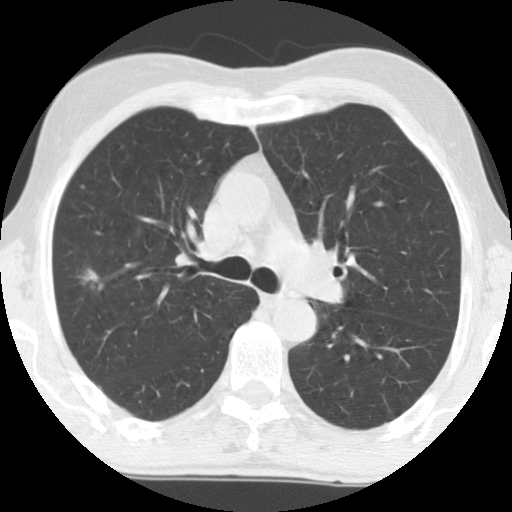
Low-dose screening chest CT, axial slice. Baseline annual screen. Lung window (W 1500 / L -600 HU). Slice 45 of 133 in the series. Male participant, aged 69 years at enrolment.
• Expert-annotated lung lesion, bounding box [x1, y1, x2, y2] px = [57, 256, 116, 311].
• Screening reader's record for this exam (one nodule recorded; not confirmed to be the boxed lesion): non-calcified nodule or mass ≥4 mm, right upper lobe, 8 × 8 mm, spiculated (stellate) margins, soft tissue attenuation.
• Official screen result: positive, change unspecified: nodule(s) >= 4 mm or enlarging nodule(s), mass(es), or other non-specific abnormalities suspicious for lung cancer.
• Lung cancer was diagnosed 588 days after this screen: mucinous adenocarcinoma, right upper lobe, moderately differentiated (G2), stage IA (AJCC 6th edition), 11 mm at pathology.